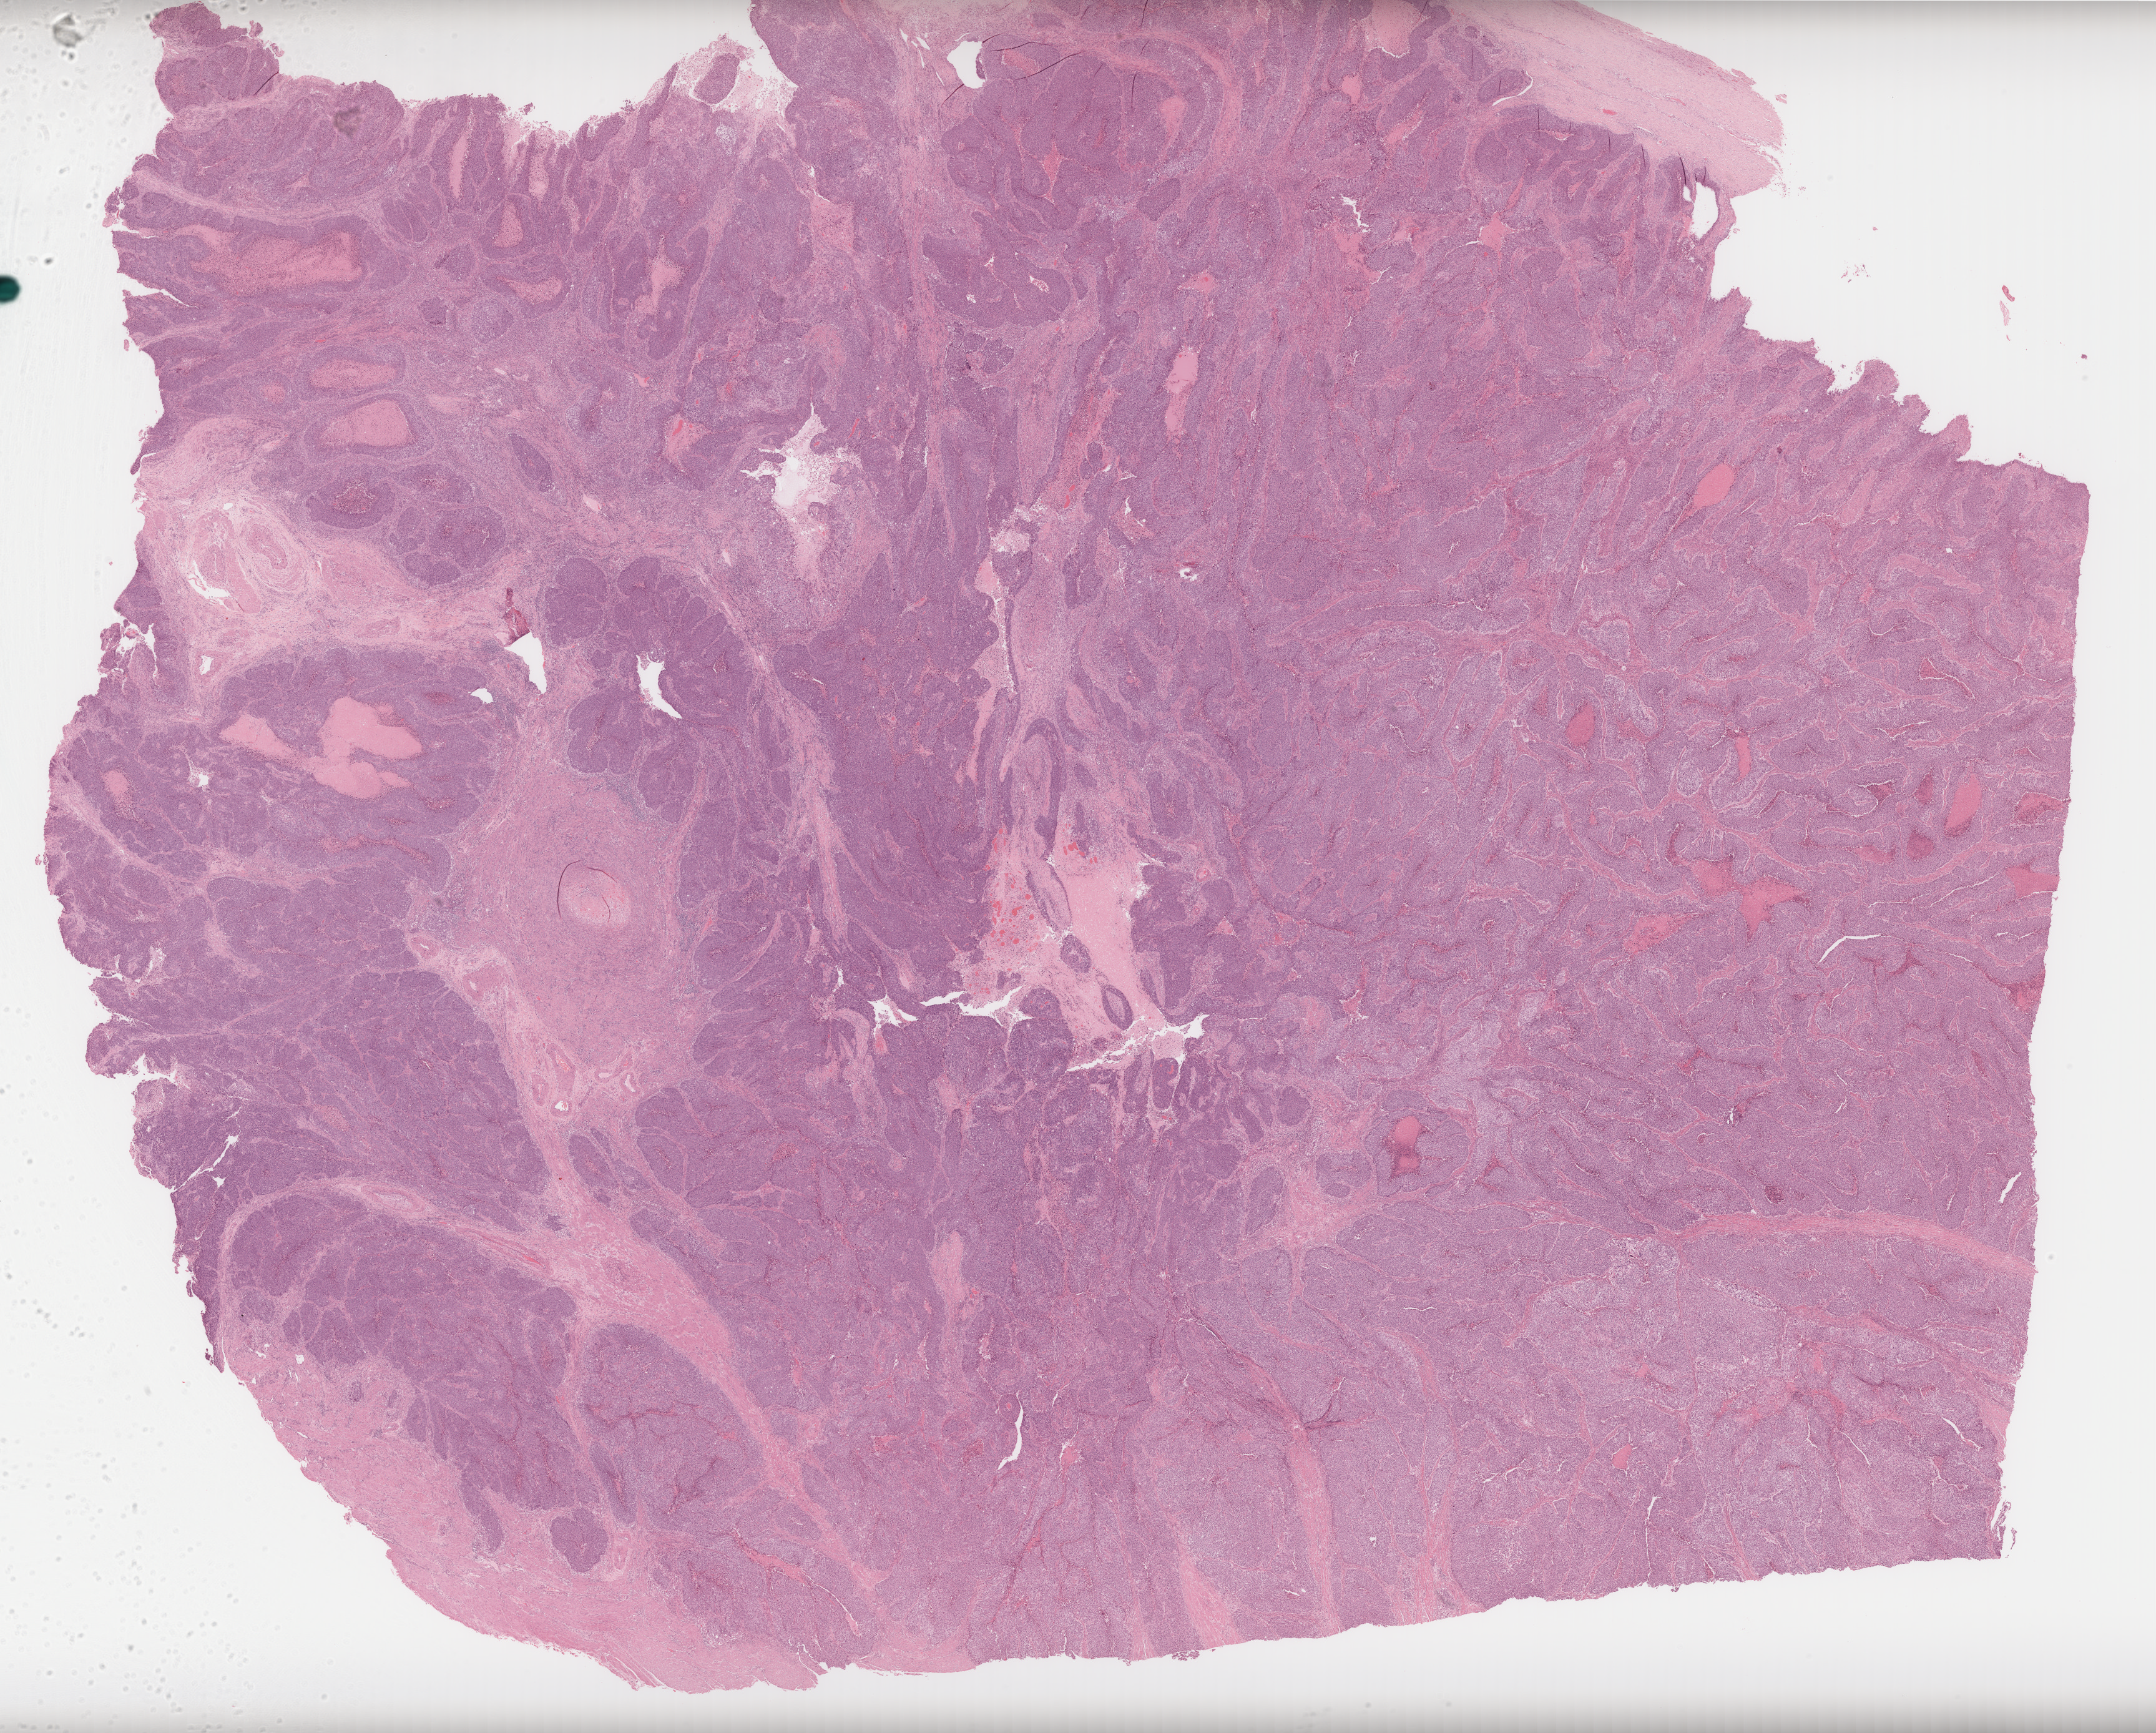
H&E-stained whole-slide image, whole scanned area (about 27.8 x 22.4 mm, acquisition: 40x scan) shown as a low-resolution overview, formalin-fixed paraffin-embedded (FFPE) diagnostic section, uterus, primary tumour sample. Female, age 36 years at initial diagnosis. Histologic grade: G3 (poorly differentiated).
Pathologic diagnosis: Endometrioid adenocarcinoma, NOS (endometrium). Lymph nodes positive (case pathology): 0 of 10 examined. FIGO stage: IIIA.